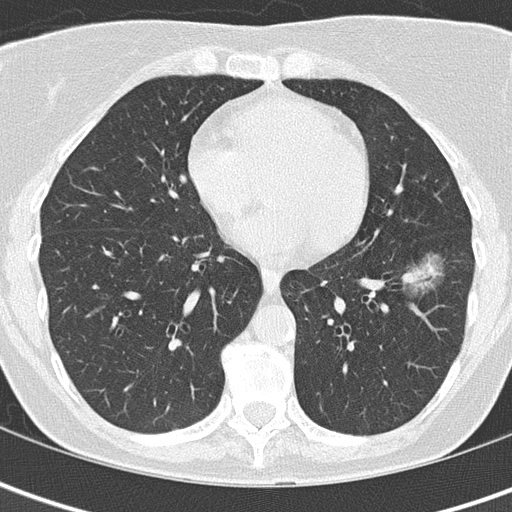
Axial slice from a low-dose chest CT screening exam; first (baseline) screen; lung window (W 1500 / L -600 HU); slice 89 of 149 in the series. Female, age 61 years at enrolment.
Lesion marked by an expert reader, box from (x=381, y=248) to (x=455, y=306) px. Screening reader's record for this exam (one nodule recorded; not confirmed to be the boxed lesion): non-calcified nodule or mass ≥4 mm, left lower lobe, 29 × 16 mm, ground glass attenuation.